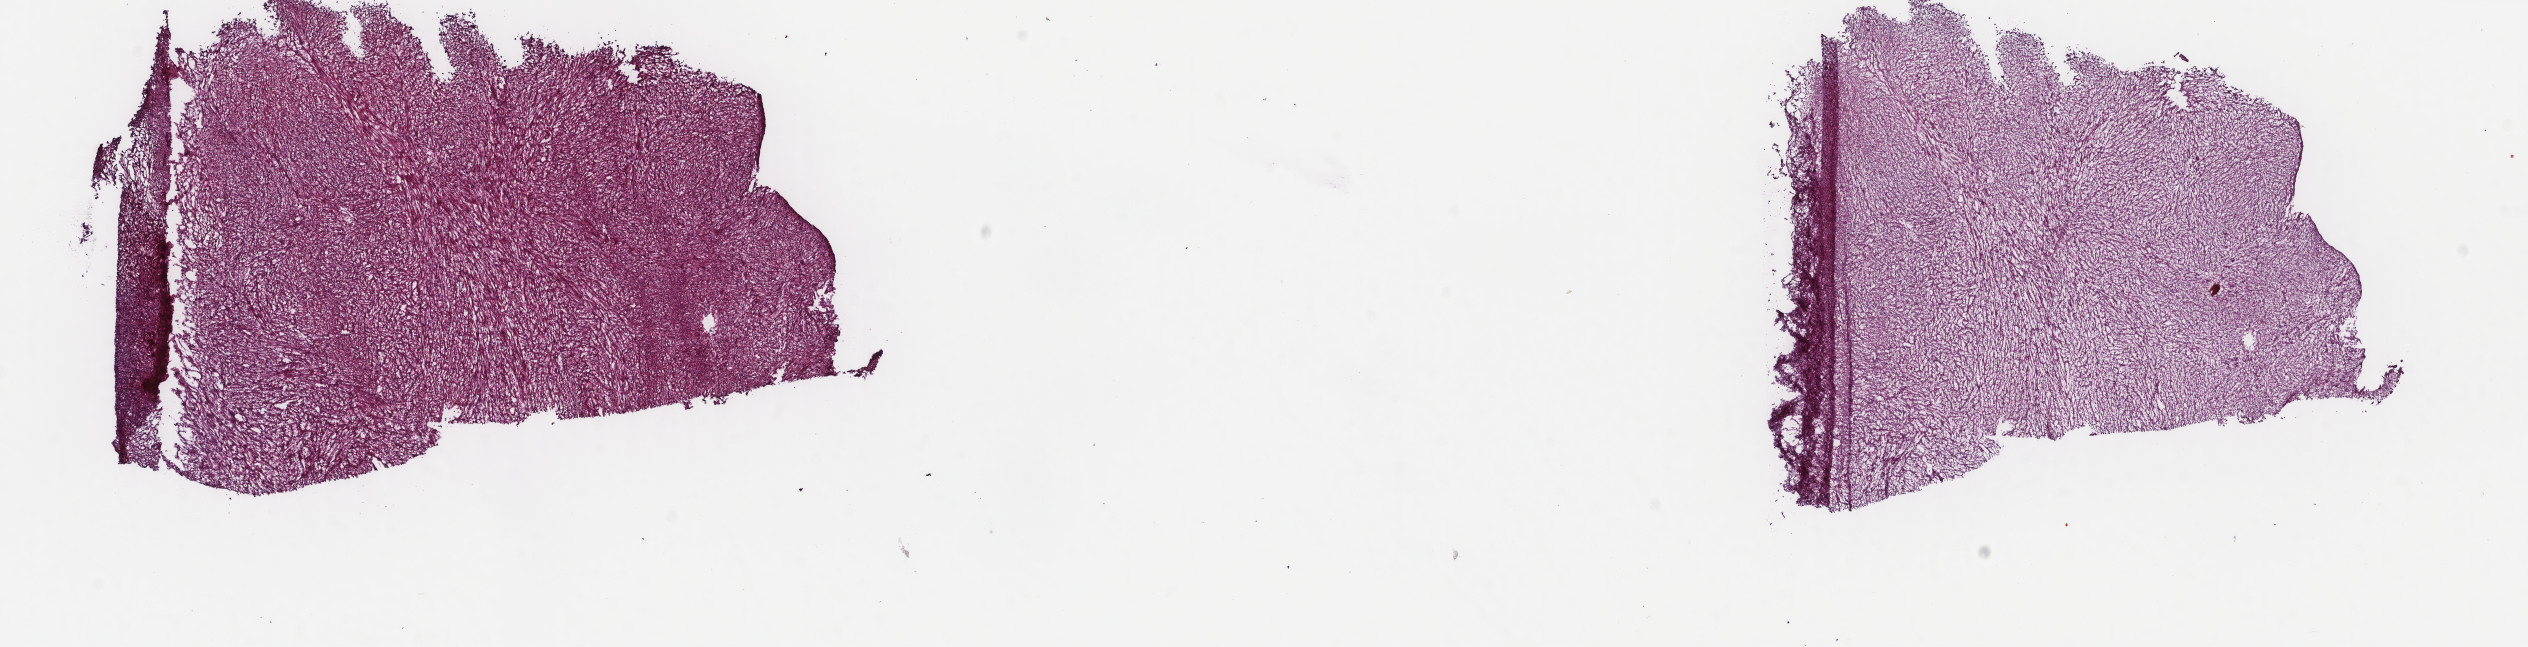
H&E-stained whole-slide image, shown as a low-resolution overview of the whole scanned area (about 20.1 x 5.1 mm, slide scanned at 40x), frozen section from the top of the tissue portion, sample: primary tumour, retroperitoneum and peritoneum. Patient: female, age at initial diagnosis 37 years. Pathologist review of this section (percent, as recorded): tumour cells 100%, tumour nuclei 94%, normal cells 0%, stromal cells 0%, necrosis 0%. Inflammatory infiltration, as recorded: lymphocyte infiltration 0%, monocyte infiltration 0%, neutrophil infiltration 0%.
Histologic diagnosis: Leiomyosarcoma, NOS (retroperitoneum).